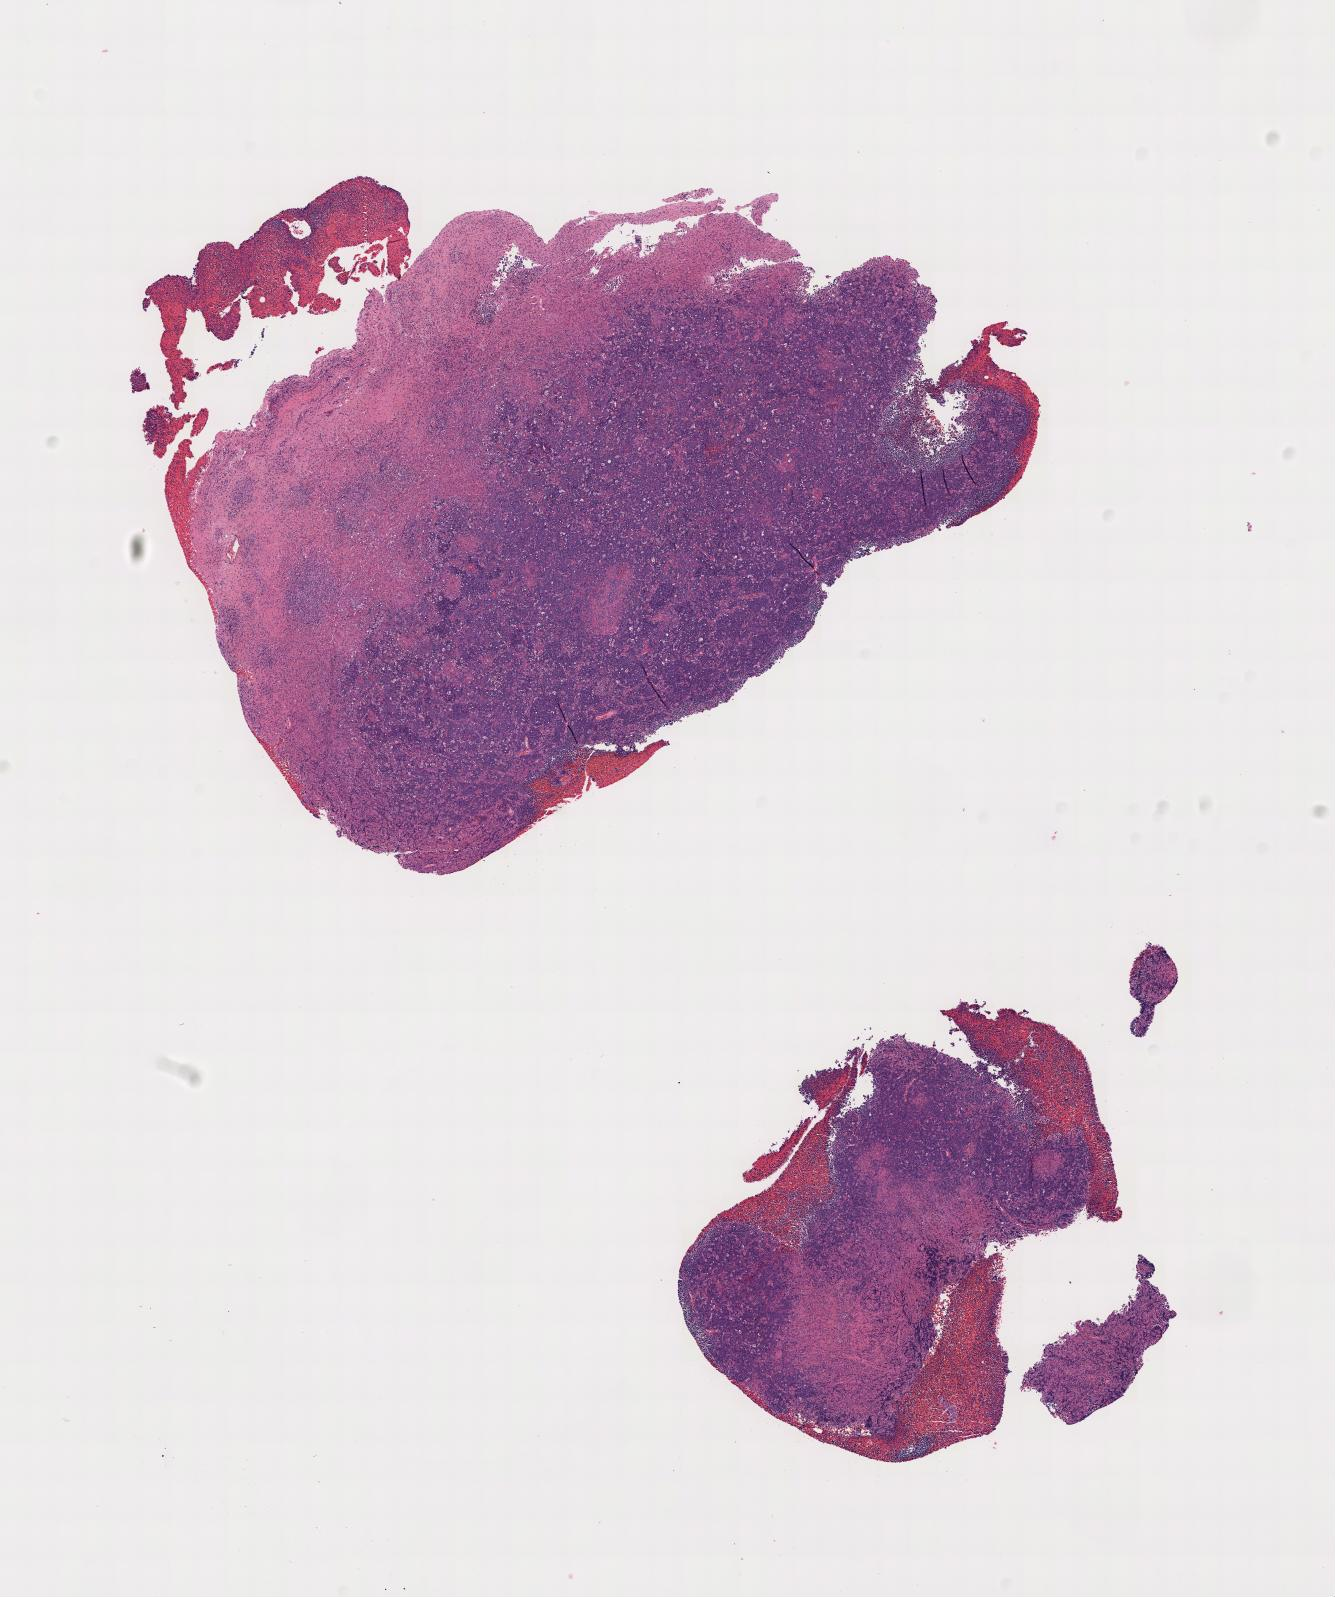
Digitized hematoxylin and eosin (H&E)-stained section, shown as a low-resolution overview of the whole scanned area. Tumor tissue. Anatomic site: lymph node of head and neck. Male patient; age at initial diagnosis 5 years.
• diagnosis: Burkitt lymphoma, NOS